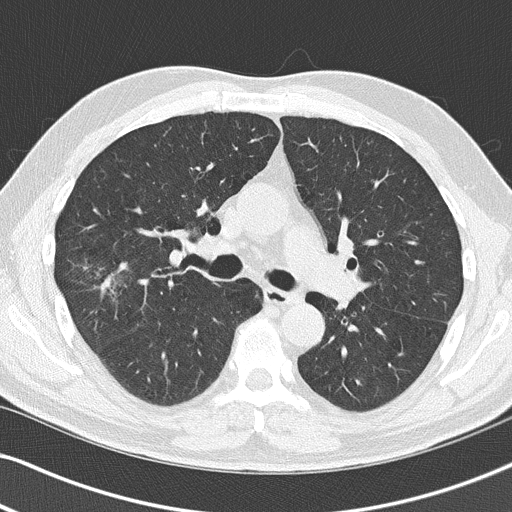
Low-dose screening chest CT, axial slice, first (baseline) screen, lung window (W 1500 / L -600 HU), 2 mm slice thickness, slice 62 of 140 in the series, 512 × 512 image matrix, field of view 330 × 330 mm. Male, age 67 years at enrolment. Former smoker at enrolment.
• Expert-annotated lung lesion, bounding box (x1, y1, x2, y2) in pixels: (69, 251, 146, 320).
• The exam's reader record, not a measurement of the box and not confirmed to be the same lesion: non-calcified nodule or mass ≥4 mm, right upper lobe, 26 × 24 mm, spiculated (stellate) margins, soft tissue attenuation.
• Official screen result: positive, change unspecified: nodule(s) >= 4 mm or enlarging nodule(s), mass(es), or other non-specific abnormalities suspicious for lung cancer.
• Later outcome: lung cancer diagnosed 49 days after this screen — squamous cell carcinoma, NOS, right upper lobe, poorly differentiated (G3), stage IA (AJCC 6th edition), 27 mm at pathology.